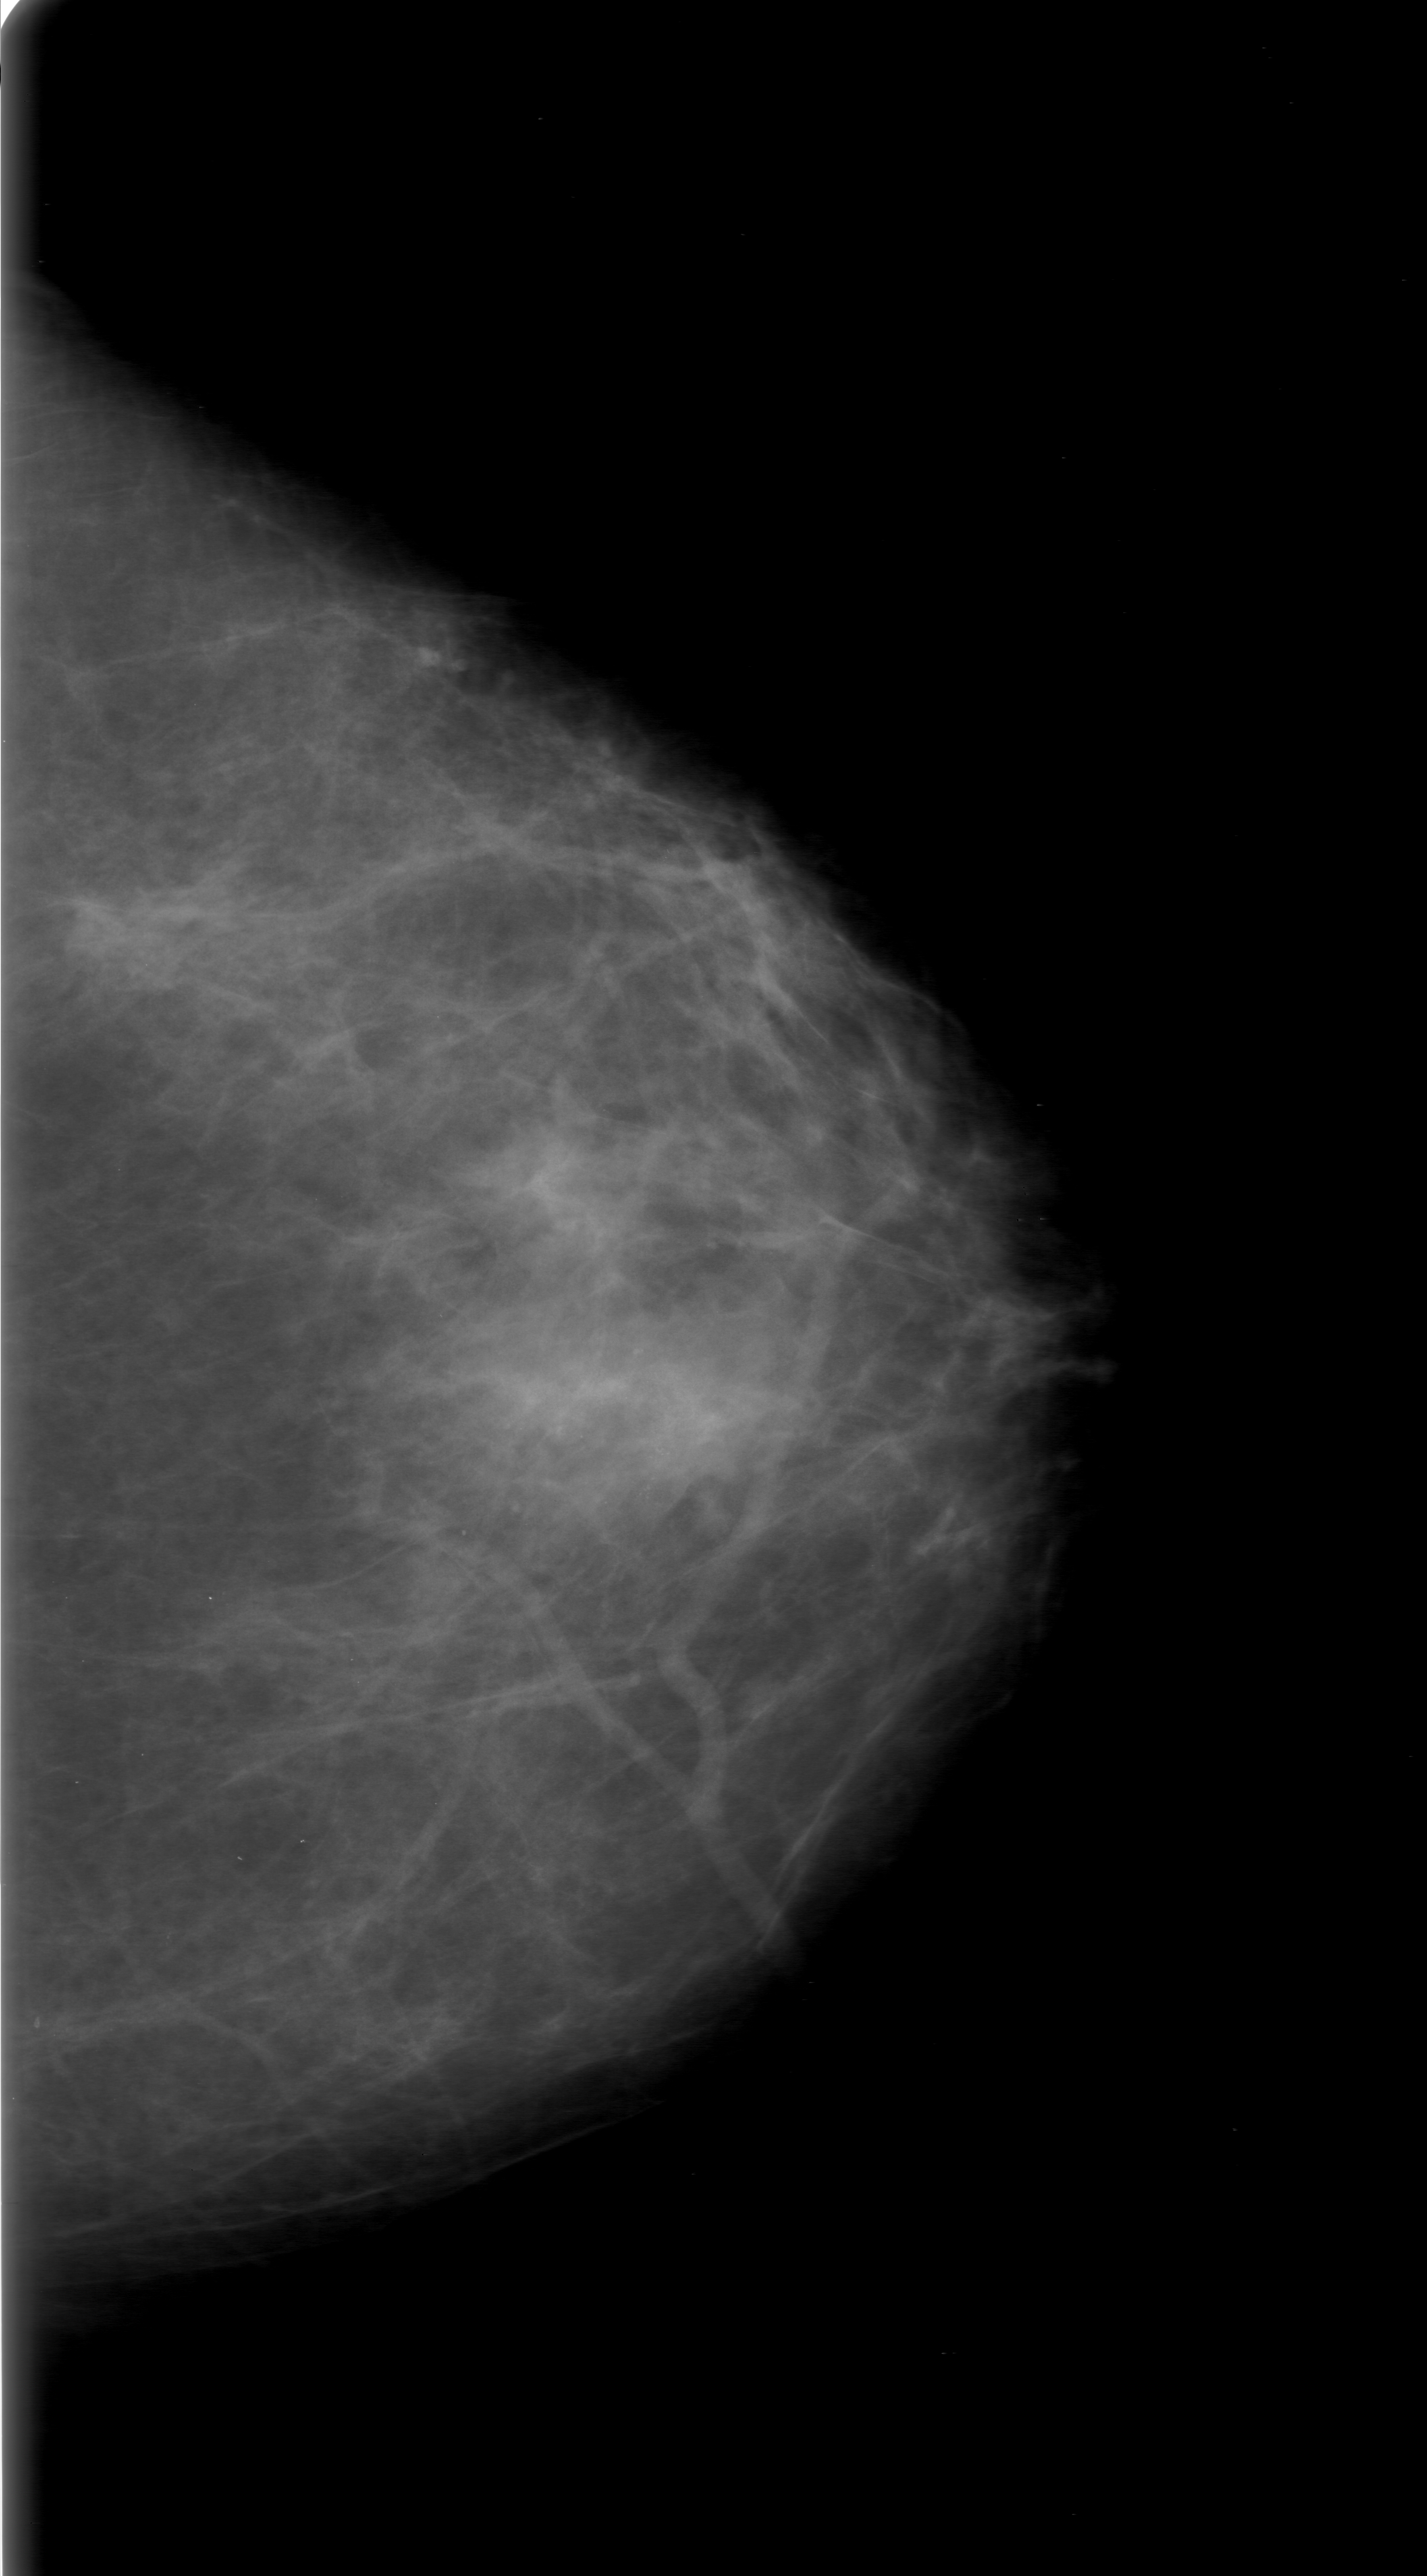
Scanned film-screen mammogram. Left breast. CC view. BI-RADS breast density category 2 (scale 1–4). 1427 × 2576 image matrix.
Expert-marked regions of interest on this film, with their recorded descriptors:
- calcifications, morphology amorphous, distribution clustered; BI-RADS assessment category 0; pathology result (as recorded, not read from the image): malignant: box from (x=511, y=1338) to (x=734, y=1536) px